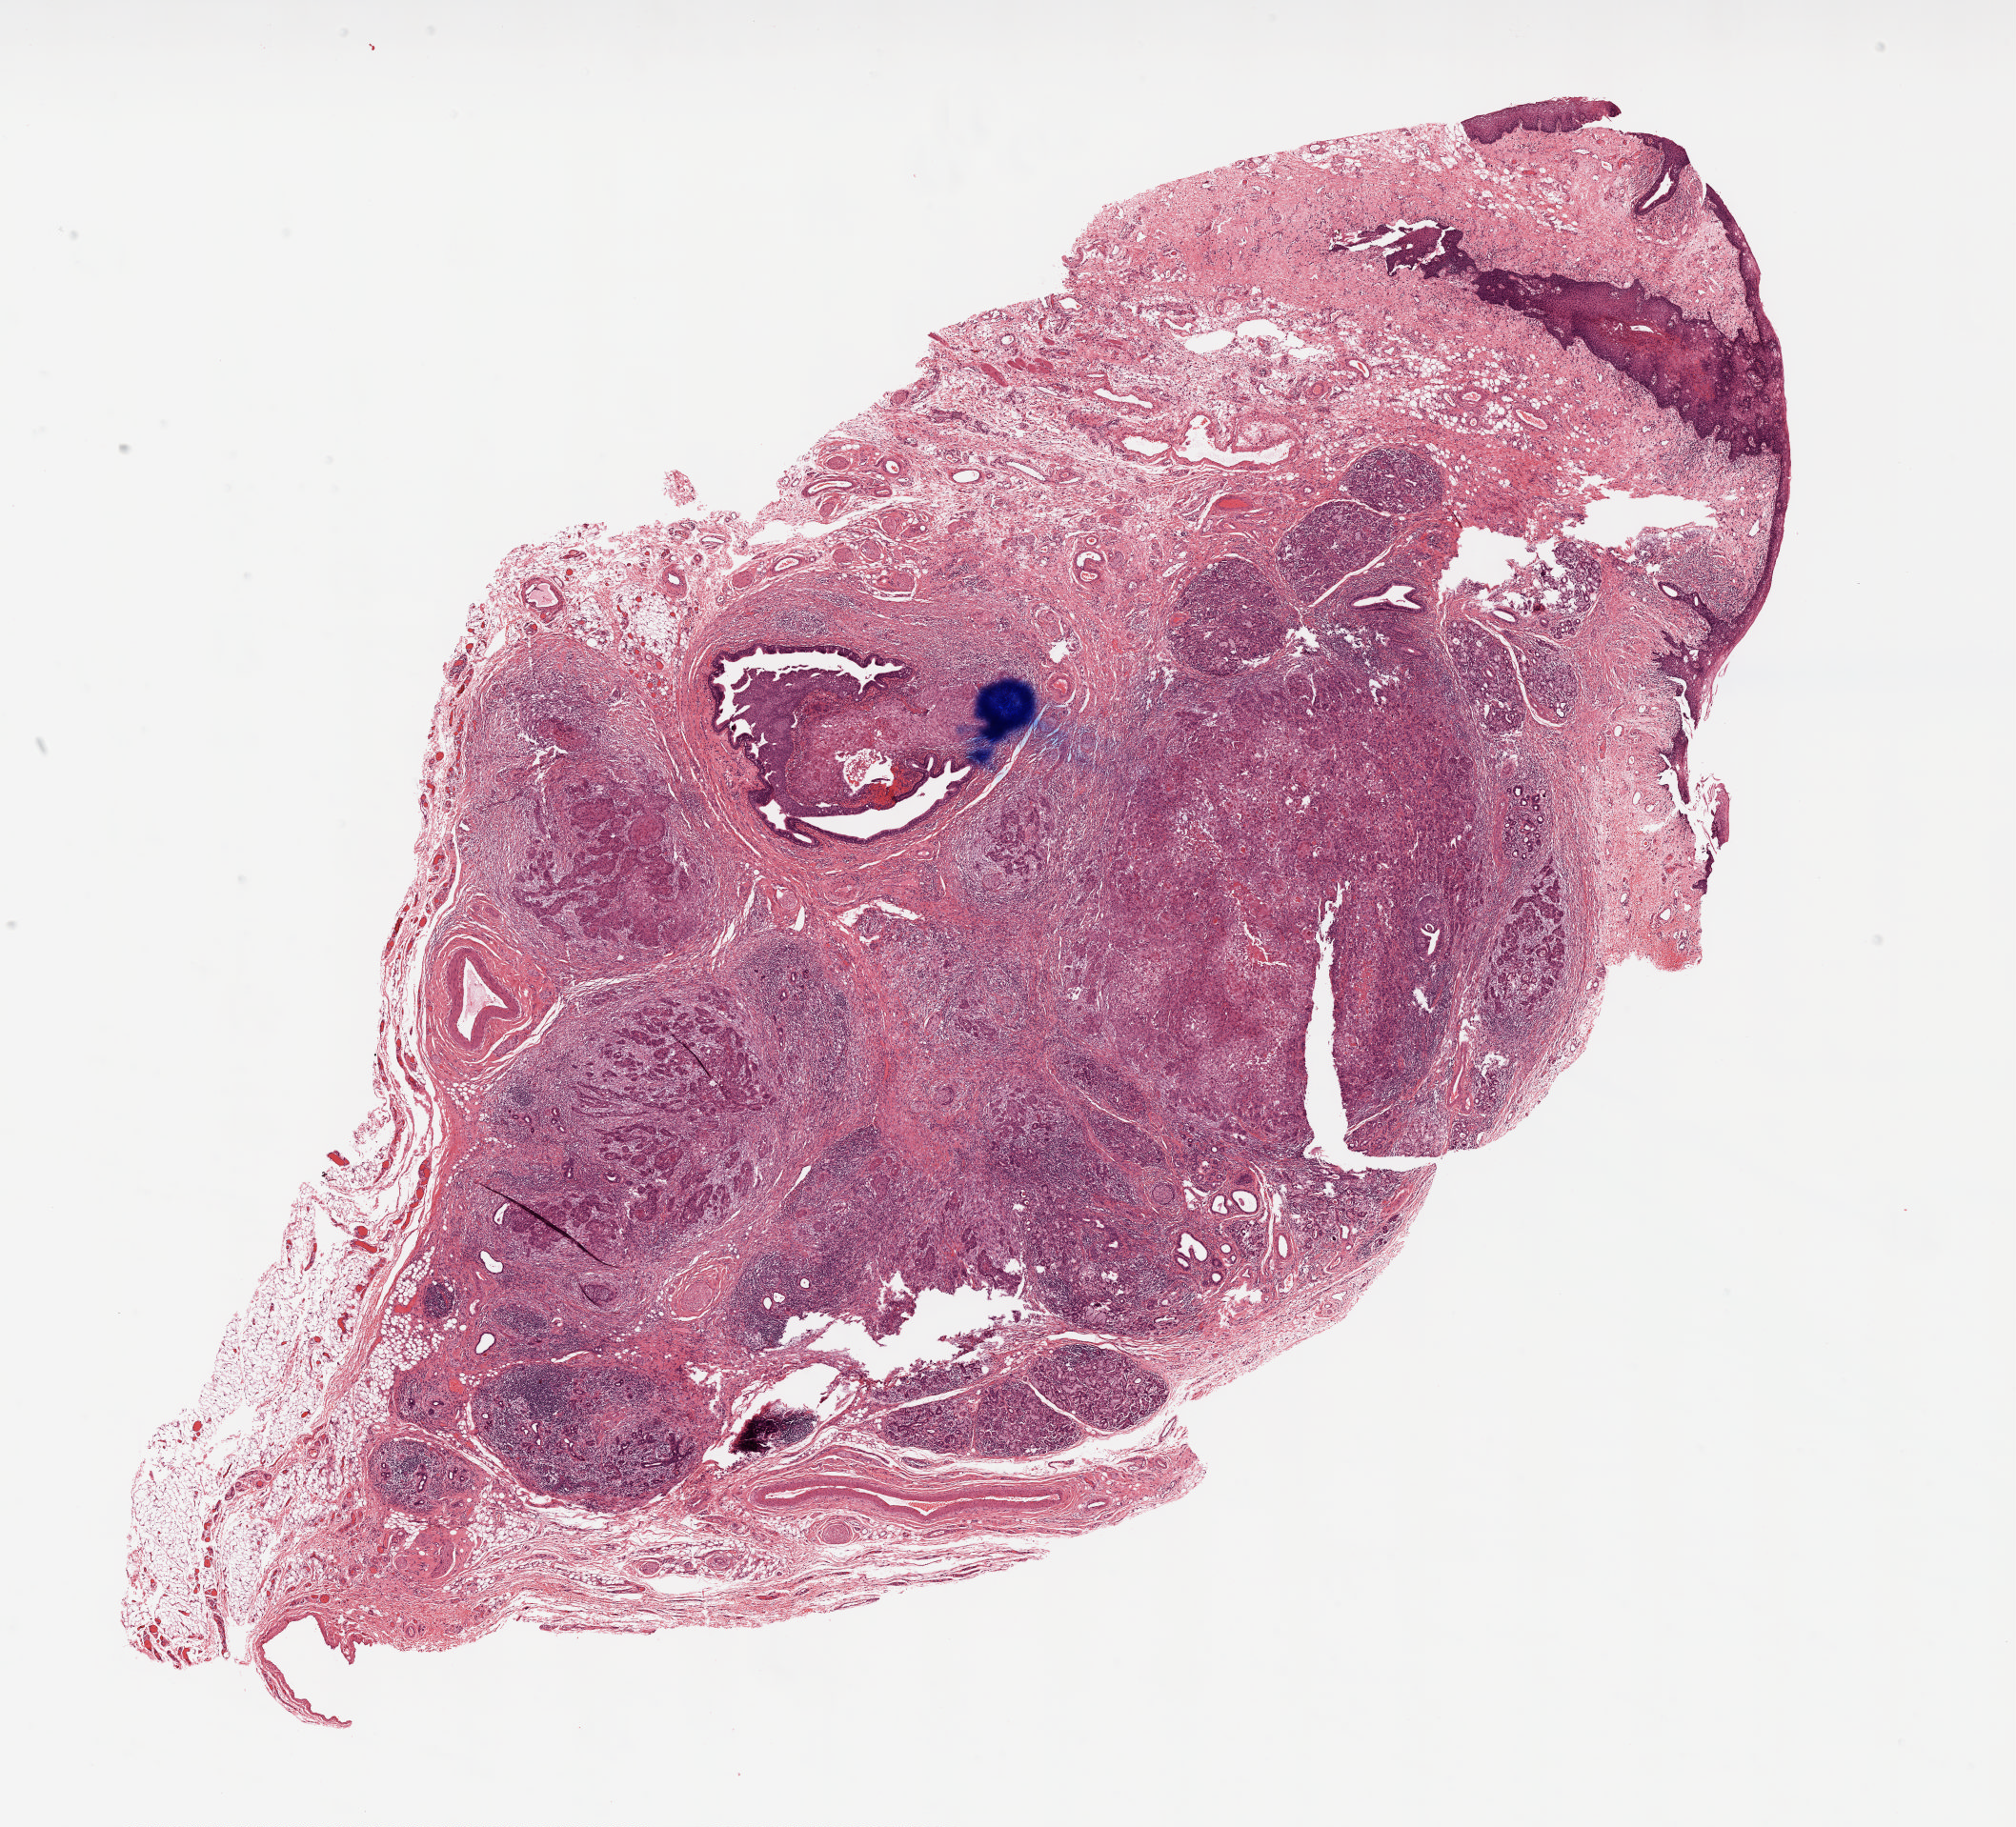
Digitized H&E-stained tissue section (whole slide) — shown as a low-resolution overview of the whole scanned area (about 17.0 x 15.4 mm, slide scanned at 20x). Formalin-fixed paraffin-embedded (FFPE) diagnostic section. Sample: primary tumour, head and neck. Male patient; age at initial diagnosis 59 years. Histologic grade: G2 (moderately differentiated).
Pathologic diagnosis: Squamous cell carcinoma, keratinizing, NOS (floor of mouth, NOS). TNM: T1 N1 M0. AJCC pathologic stage: III (7th edition).